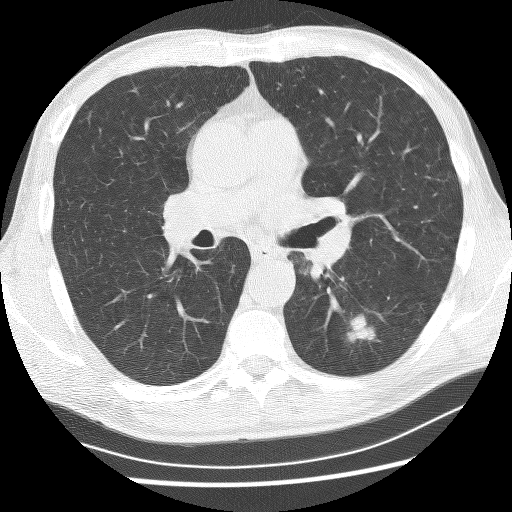
Low-dose screening chest CT, one axial slice; position 141 of 253 along the scan axis; reconstruction kernel BONE; 120 kVp; lung window (W 1500 / L -600 HU); 2.5 mm slice thickness; 512 × 512 image matrix.
Structures marked on this image (outlined manually by an expert reader):
- lesion 1 (tumor, lower lobe of left lung): box from (x=348, y=315) to (x=375, y=342) px